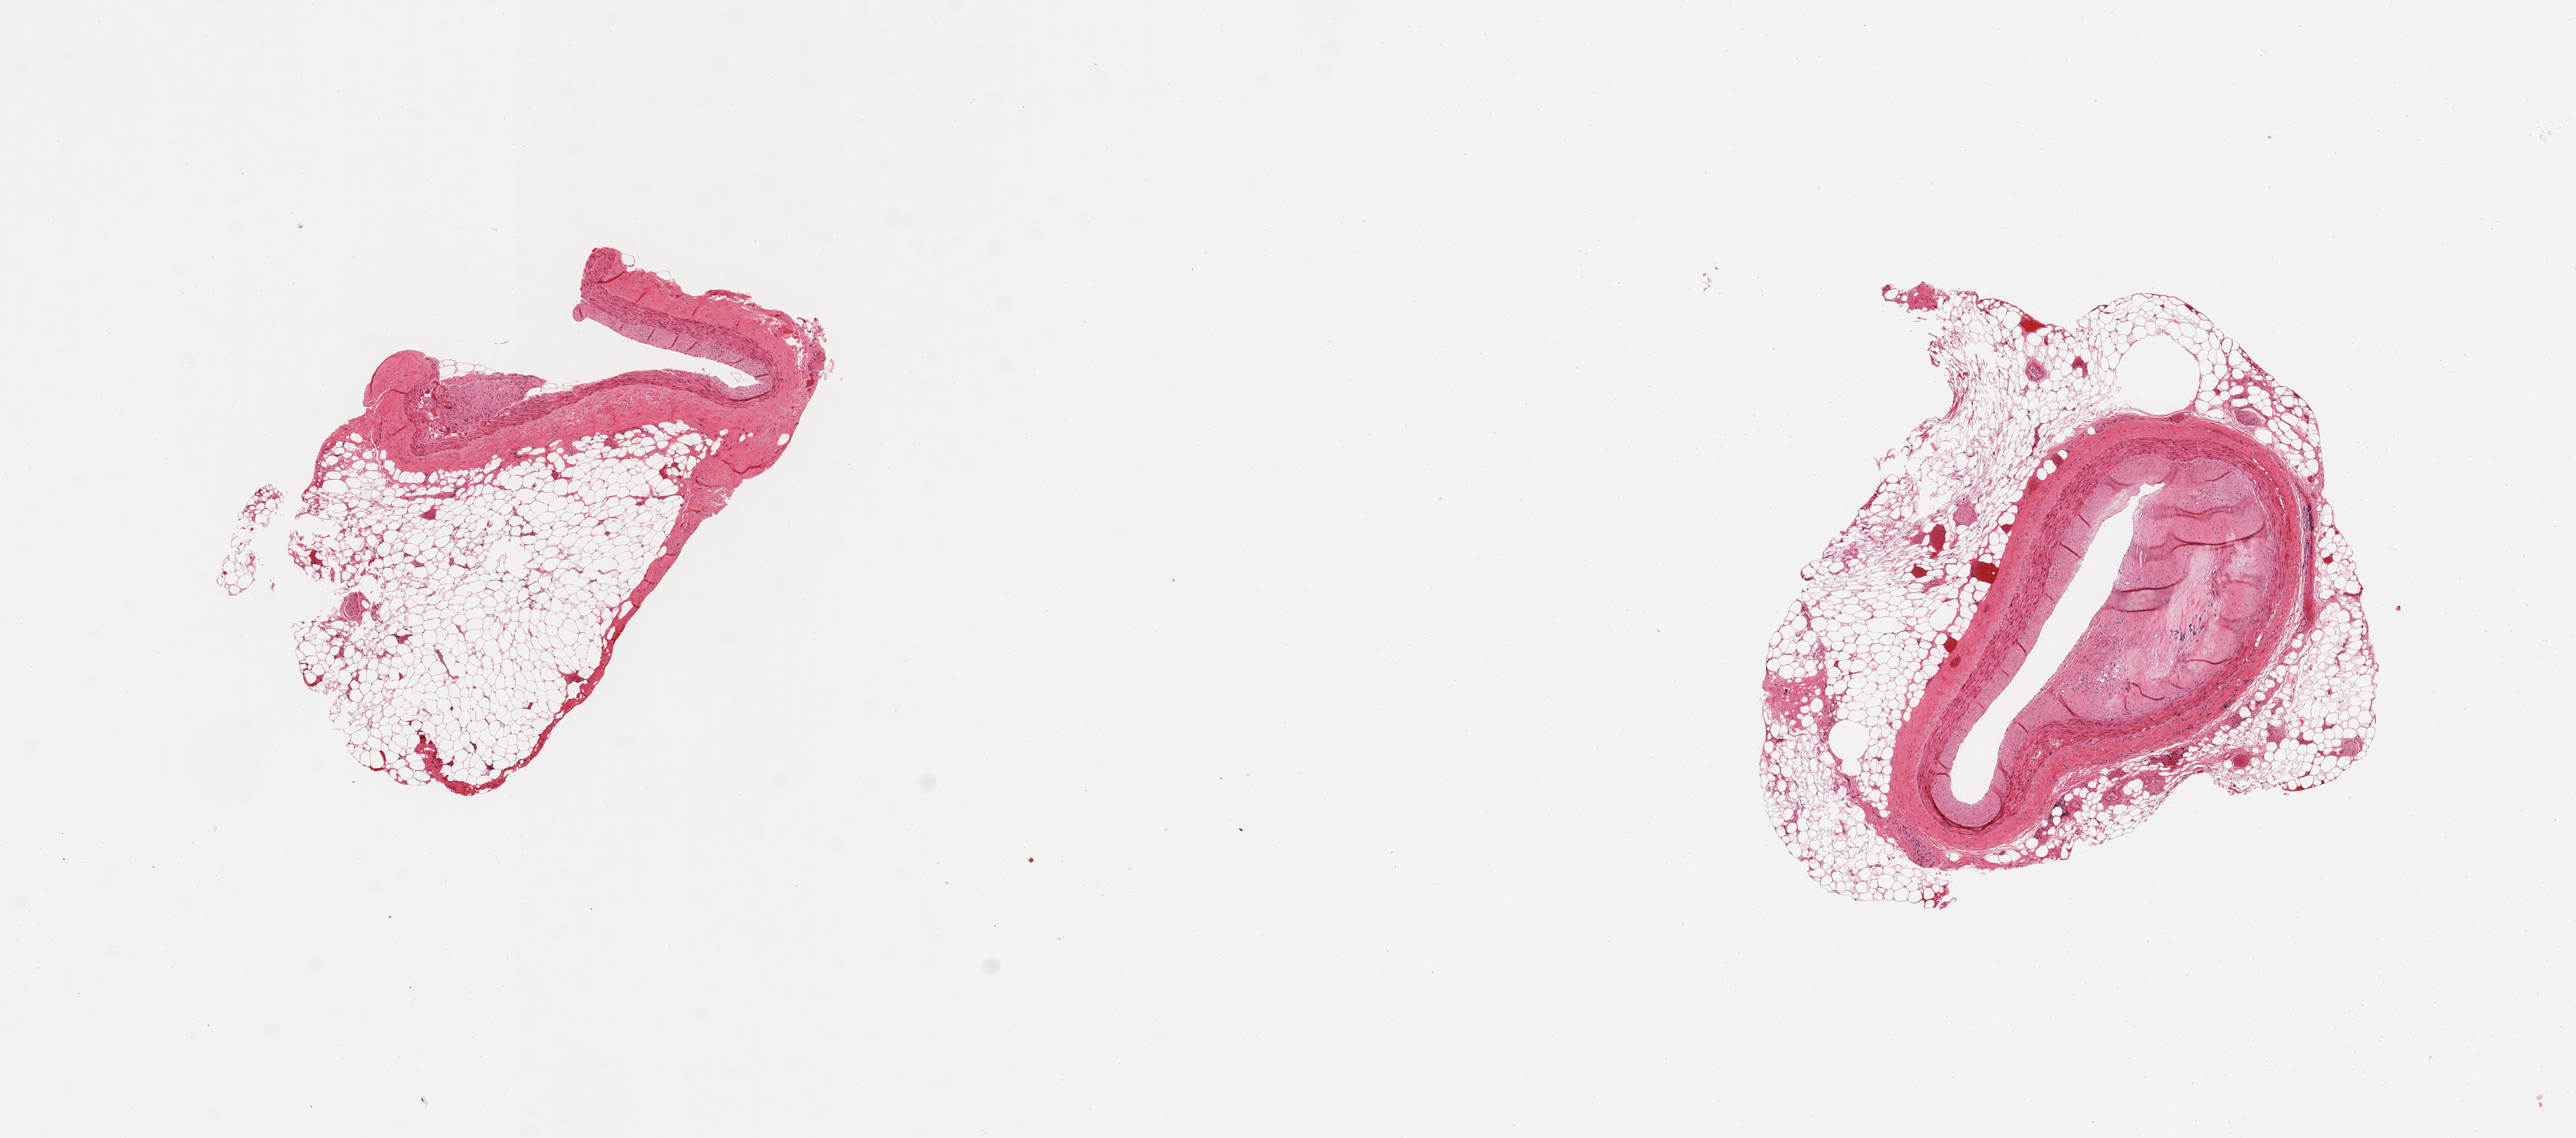
Hematoxylin and eosin (H&E) whole-slide image, brightfield, a low-resolution overview of the entire scanned area, about 14.8 x 6.5 mm, PAXgene-fixed paraffin-embedded (PFPE) section, section of coronary artery (target tissue), tissue donor sample. Donor: male.
• pathologist's review note for this sample: 2 pieces; 1 piece with eccentric atherosclerotic plaque with ~75% luminal compromise and up to 1.3mm attached external fat, second piece is tangentially cut, both include >50% fat